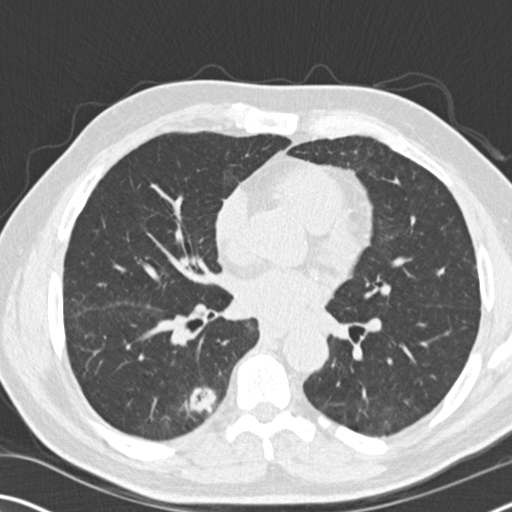
Low-dose screening chest CT, axial slice, baseline annual screen, lung window (W 1500 / L -600 HU), 2 mm slice thickness, standard (soft-tissue) reconstruction kernel (B30f), 120 kVp, slice 88 of 169 in the series. Male participant, aged 71 years at enrolment. Current smoker at enrolment.
Expert-annotated lung lesion, bounding box <159,373,228,434> (left, top, right, bottom; pixels). The screening reader recorded 2 non-calcified nodules or masses ≥4 mm on this exam (right lower lobe, left lower lobe); which of them this box marks is not recorded. Official screen result: positive, change unspecified: nodule(s) >= 4 mm or enlarging nodule(s), mass(es), or other non-specific abnormalities suspicious for lung cancer. Later outcome: lung cancer diagnosed 215 days after this screen — squamous cell carcinoma, NOS, right lower lobe, moderately differentiated (G2), stage IB (AJCC 6th edition), 52 mm at pathology.